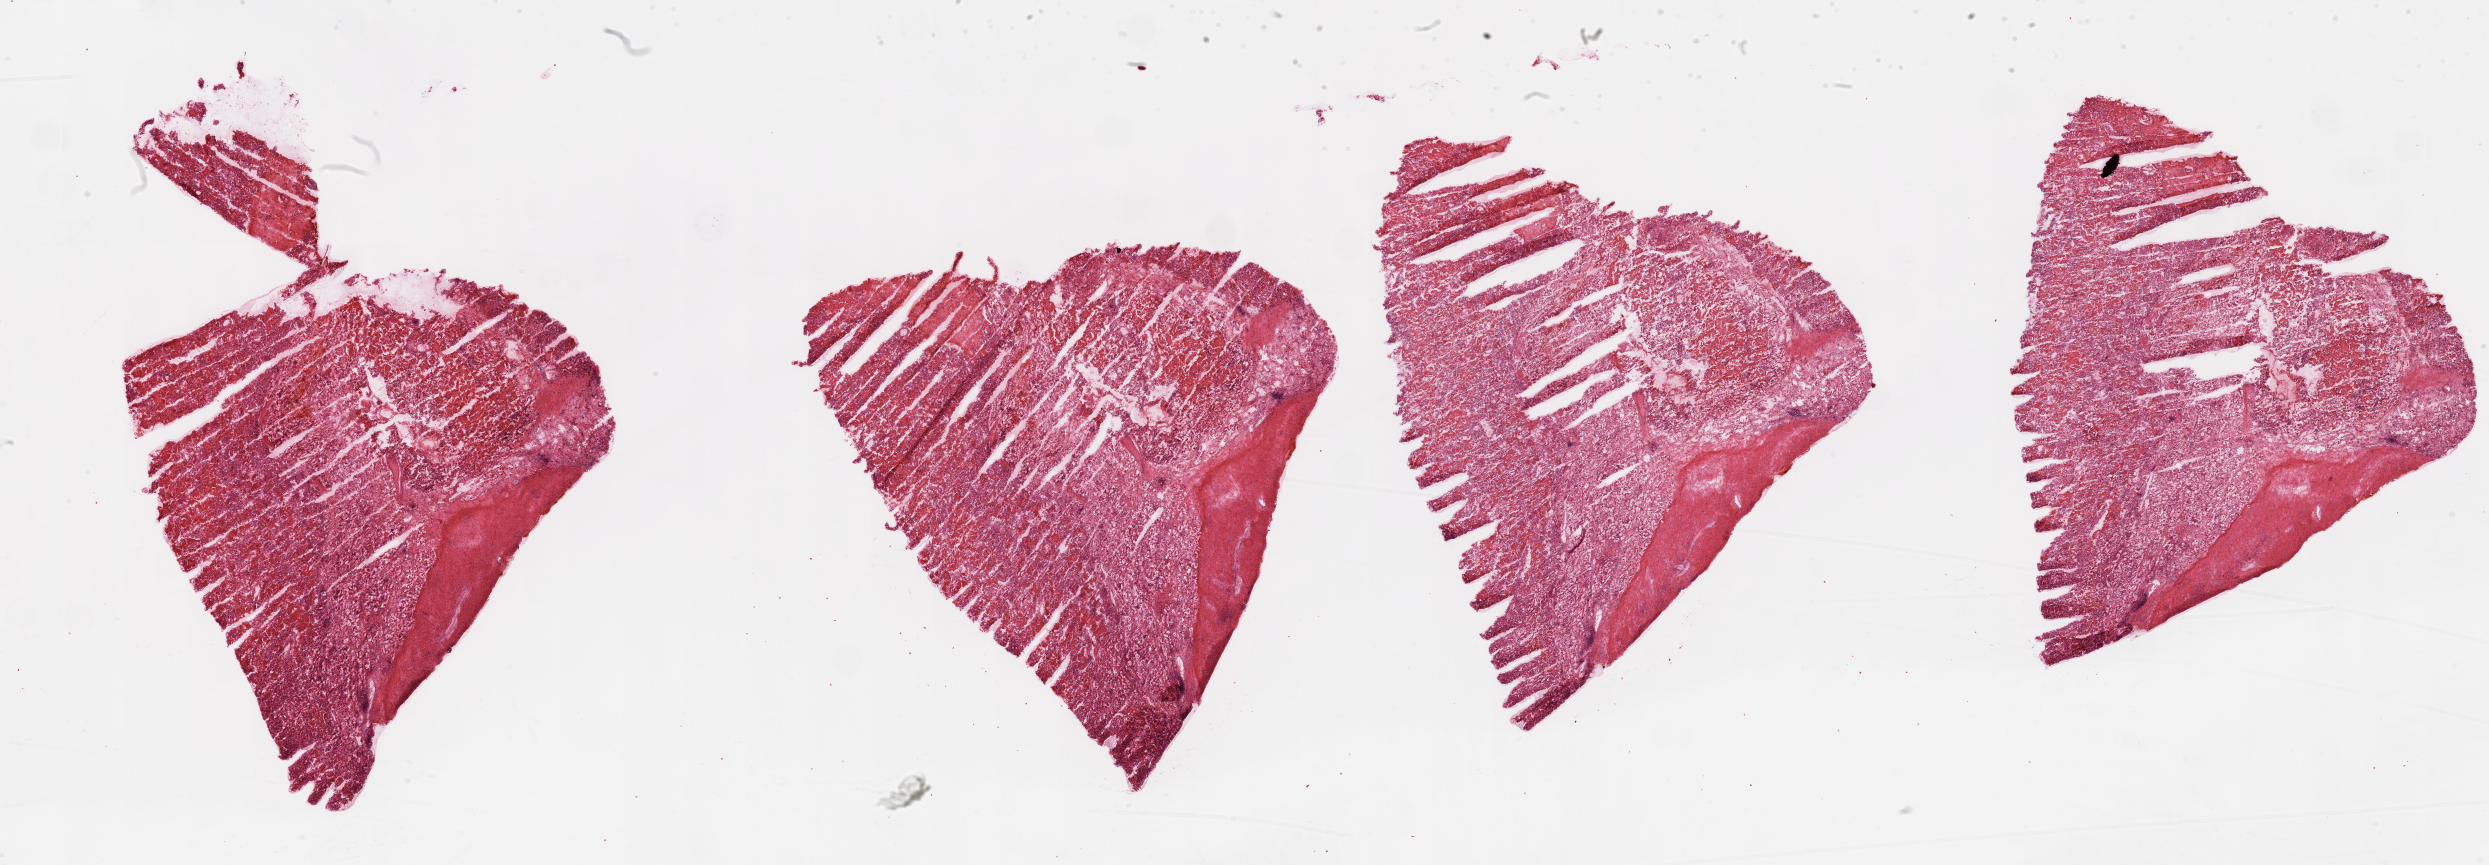
Whole-slide histology image, H&E — low-resolution overview of the scanned area, about 39.4 x 13.7 mm (acquisition: 20x scan), tumour tissue sample, sampled site: kidney. Female, 69 y/o. Composition of this section per pathologist review: tumour nuclei 90%, necrosis 10%.
Histologic diagnosis: Renal cell carcinoma, NOS.